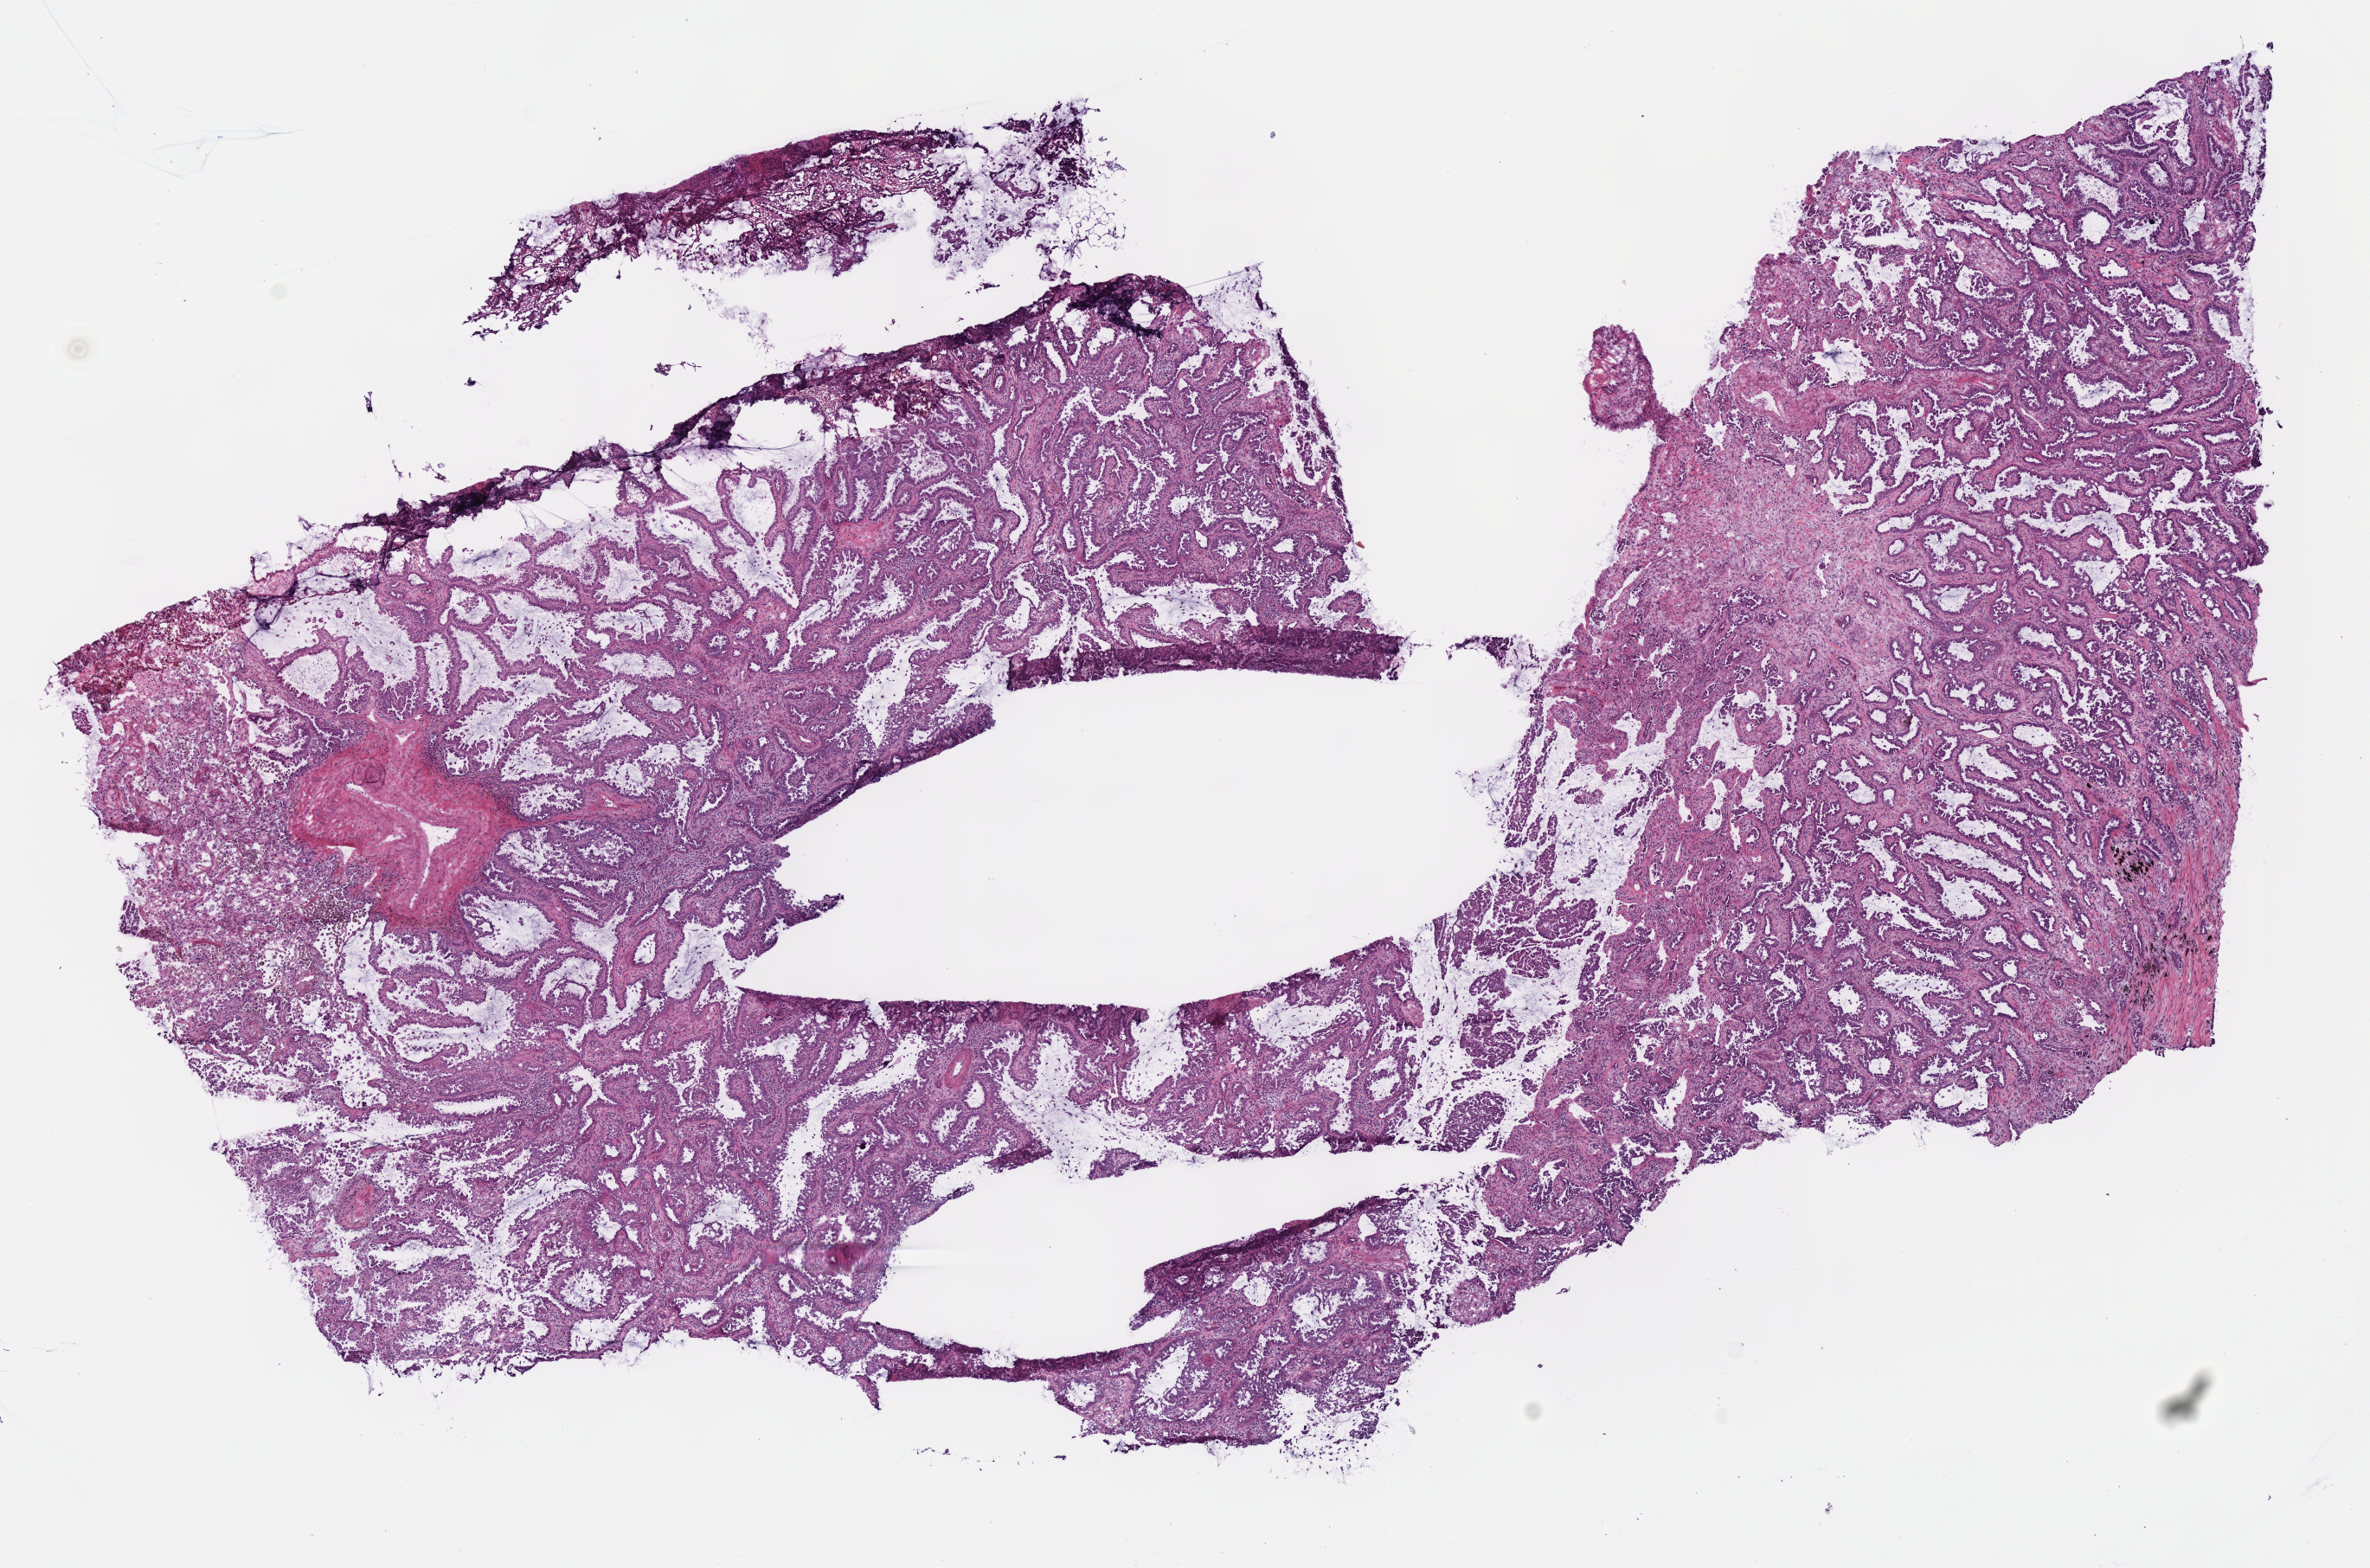
Whole-slide histology image, H&E-stained — a low-resolution overview of the entire scanned area, about 10.8 x 7.1 mm (acquisition: 40x scan). Frozen section from the bottom of the tissue portion. Lung, primary tumour sample. Female patient; age at initial diagnosis 61 years. Composition of this section per pathologist review: tumour cells 95%, tumour nuclei 80%, normal cells 0%, stromal cells 5%, necrosis 0%. Inflammatory infiltration, as recorded: lymphocyte infiltration 15%, monocyte infiltration 0%, neutrophil infiltration 0%.
TNM: T1b N2 M0. Laterality: right. Diagnosis: Adenocarcinoma with mixed subtypes (lower lobe, lung). AJCC pathologic stage: IIIA (7th edition).